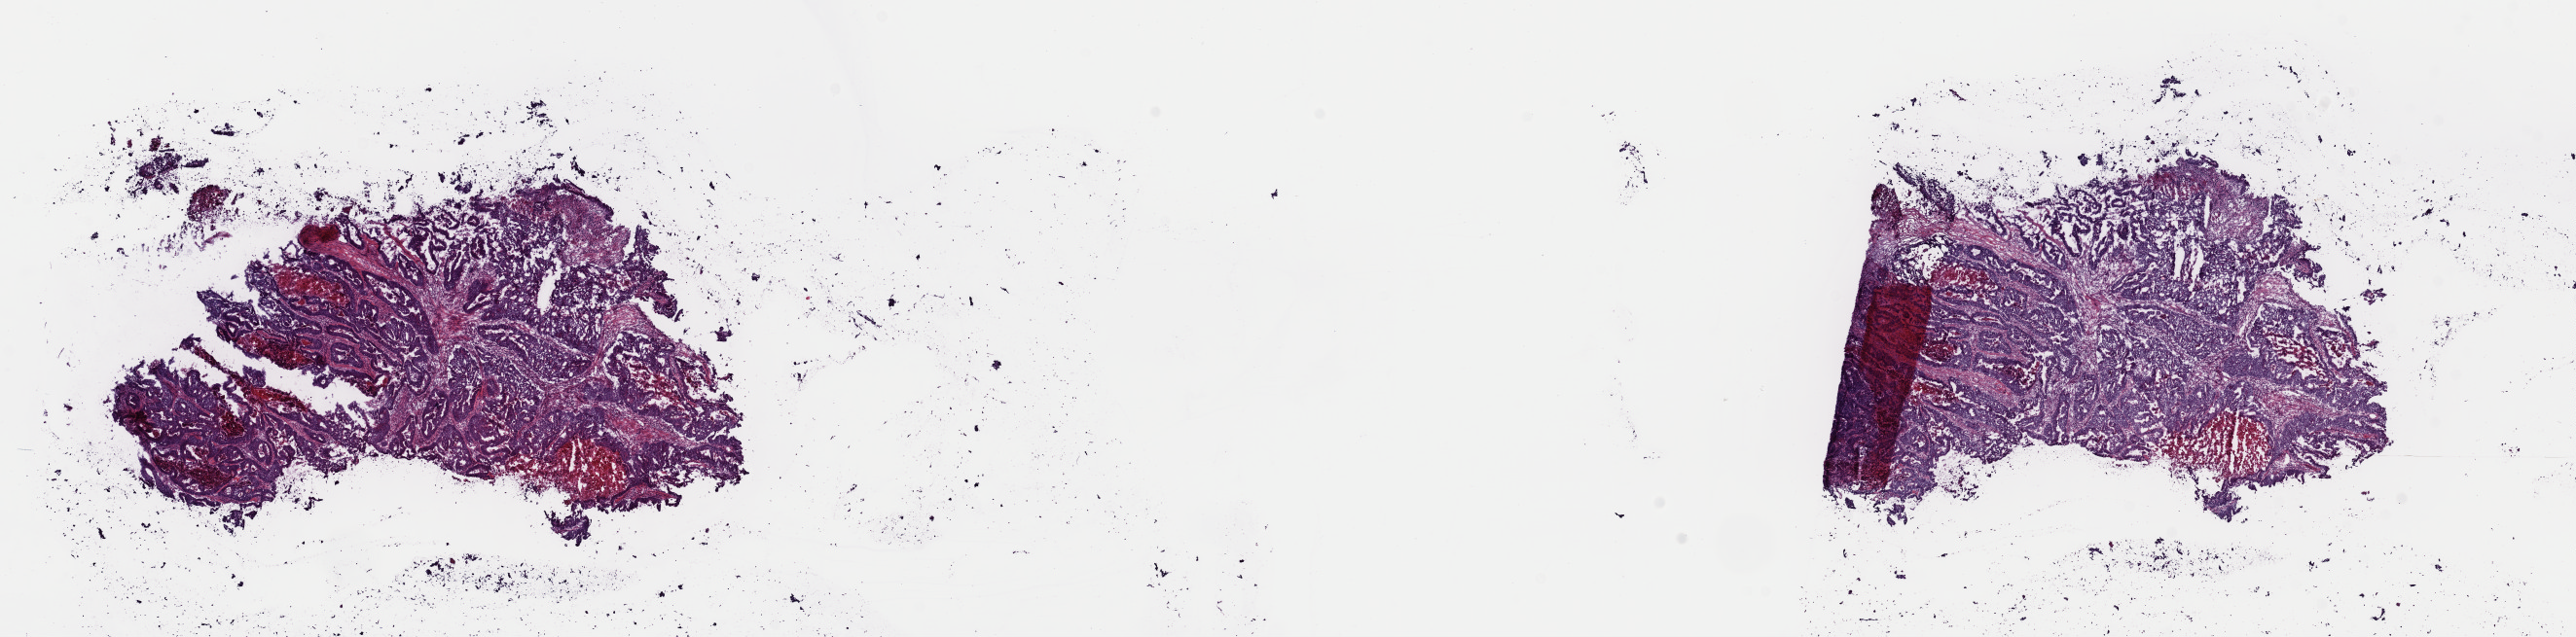
H&E-stained whole-slide image — a low-resolution overview of the entire scanned area, about 20.9 x 5.2 mm (slide scanned at 40x); frozen section from the top of the tissue portion; sample: primary tumour, colon. Patient: male, age at initial diagnosis 57 years. Slide review estimates, as recorded: tumour cells 83%, tumour nuclei 70%, normal cells 0%, stromal cells 0%, necrosis 17%. Infiltration values recorded for this section: lymphocyte infiltration 5%, monocyte infiltration 0%, neutrophil infiltration 0%.
Histologic diagnosis: Adenocarcinoma, NOS. AJCC pathologic stage: IIIB (6th edition).